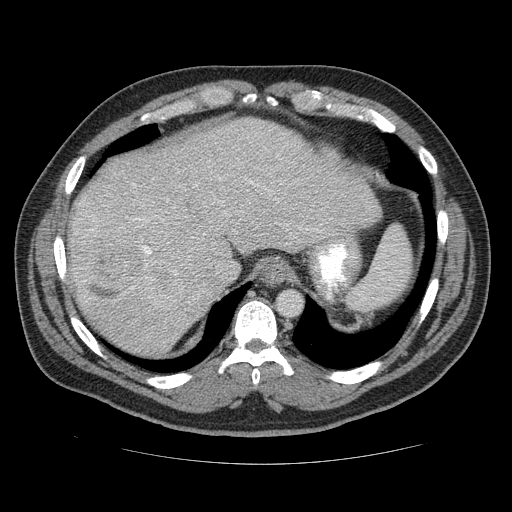
Contrast-enhanced abdominal CT (liver protocol), one axial slice. Position 98 of 113 along the scan axis. Reconstruction kernel STANDARD. 120 kVp. Soft-tissue window (W 400 / L 40 HU). 2.5 mm slice thickness. 512 × 512 image matrix, field of view 400 × 400 mm. Case-level facts recorded for this patient, not image findings: diagnosis: hepatocellular carcinoma (patient treated with transarterial chemoembolisation; whether this scan precedes or follows treatment is not stated here); TNM stage (as recorded): Stage-II; Child-Pugh class: B; tumour differentiation: moderately differentiated; tumour nodularity: multinodular.
Annotated regions visible in this slice (semi-automatically segmented with operator editing):
- abdominal aorta: box from (x=278, y=291) to (x=301, y=315) px
- liver parenchyma outside the tumour (the mass and vessels are separate outlines, so this box may not span the whole liver): (x=66, y=120)–(x=382, y=352)
- mass: (x=71, y=211)–(x=180, y=305)
- liver vessels: (x=142, y=199)–(x=190, y=265)